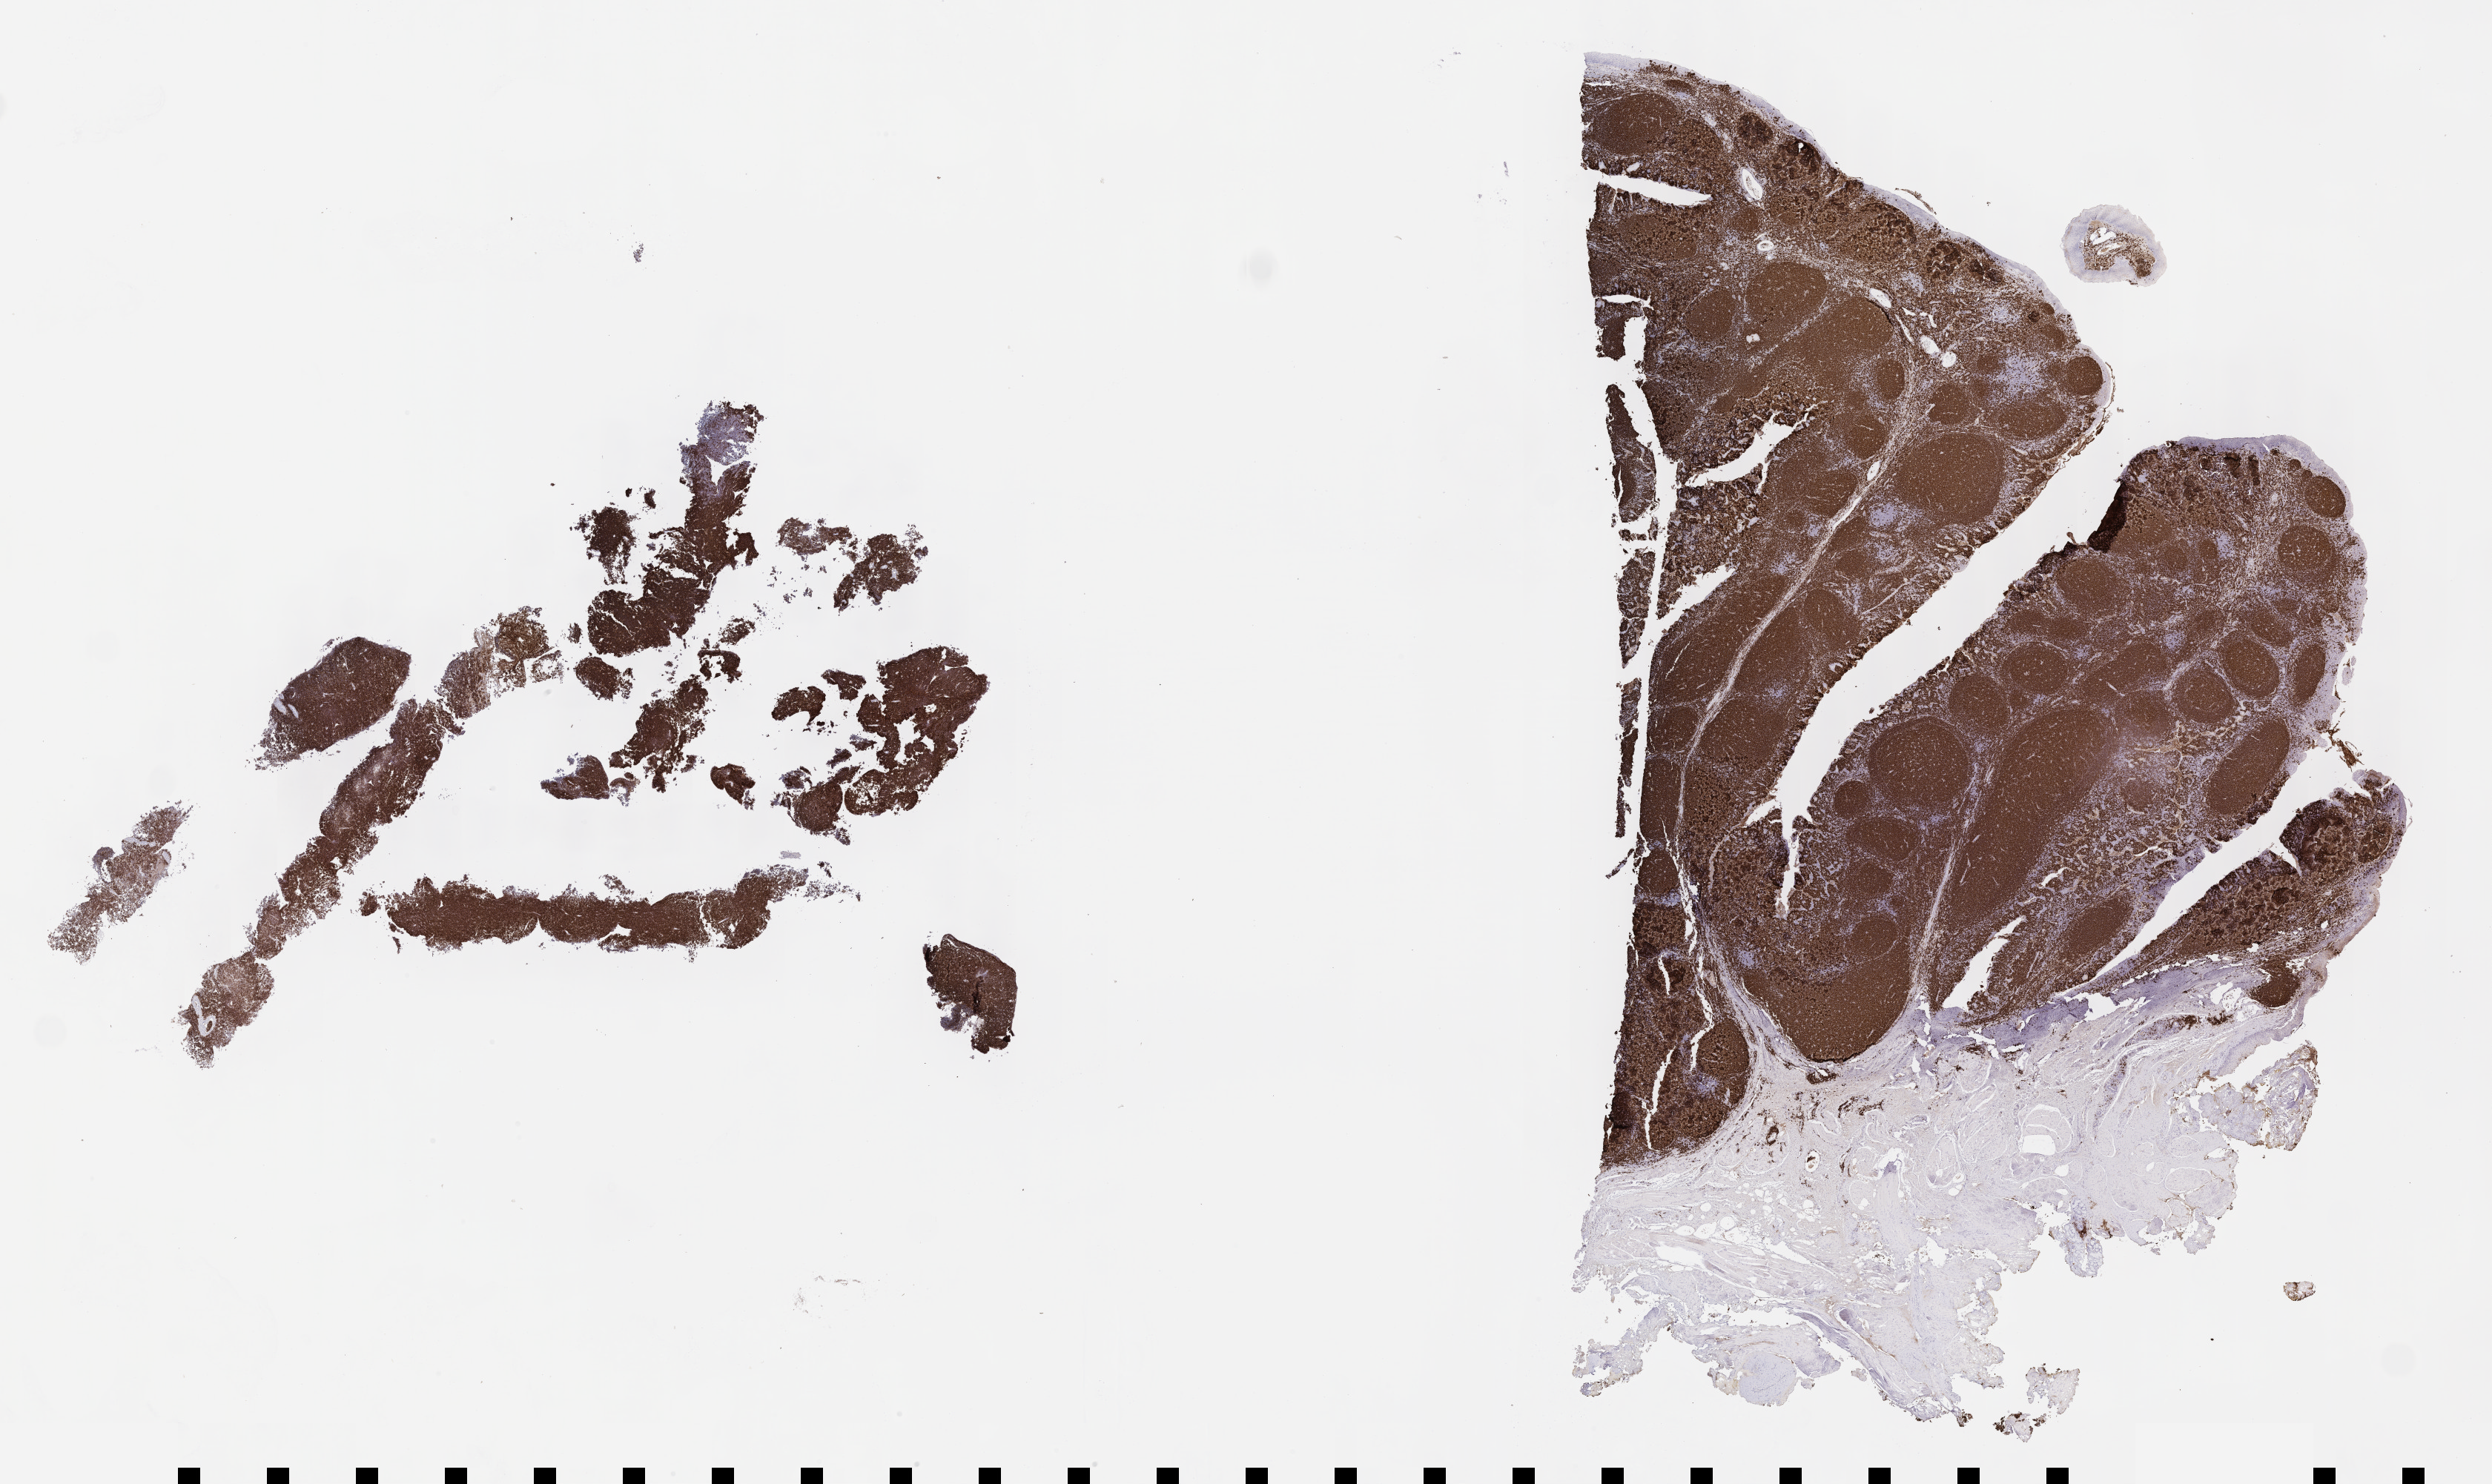
IHC for CD20, whole-slide image — shown as a low-resolution overview of the whole scanned area (about 27.2 x 16.2 mm), specimen: tumor tissue, site: kidney. Patient: male, age at initial diagnosis 3 years.
- histologic diagnosis: Burkitt lymphoma, NOS